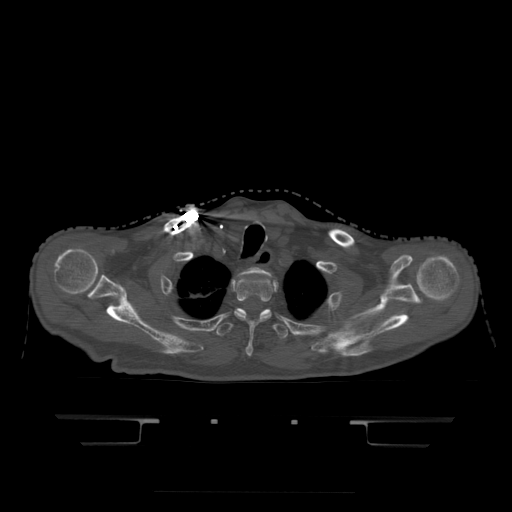
CT including the spine, one axial slice. Position 382 of 522 along the scan axis. Bone window (W 1800 / L 400 HU). 1.25 mm slice thickness. 512 × 512 image matrix, field of view 436 × 436 mm. Patient age 68 years. Case-level facts recorded for this patient, not image findings: primary cancer: urothelial.
Structures marked on this image (semi-automatically segmented with operator editing):
- T1 vertebra: bounding box [x1, y1, x2, y2] px = [240, 267, 268, 275]
- T2 vertebra: [235, 276, 273, 357]
- T3 vertebra: [216, 309, 288, 340]